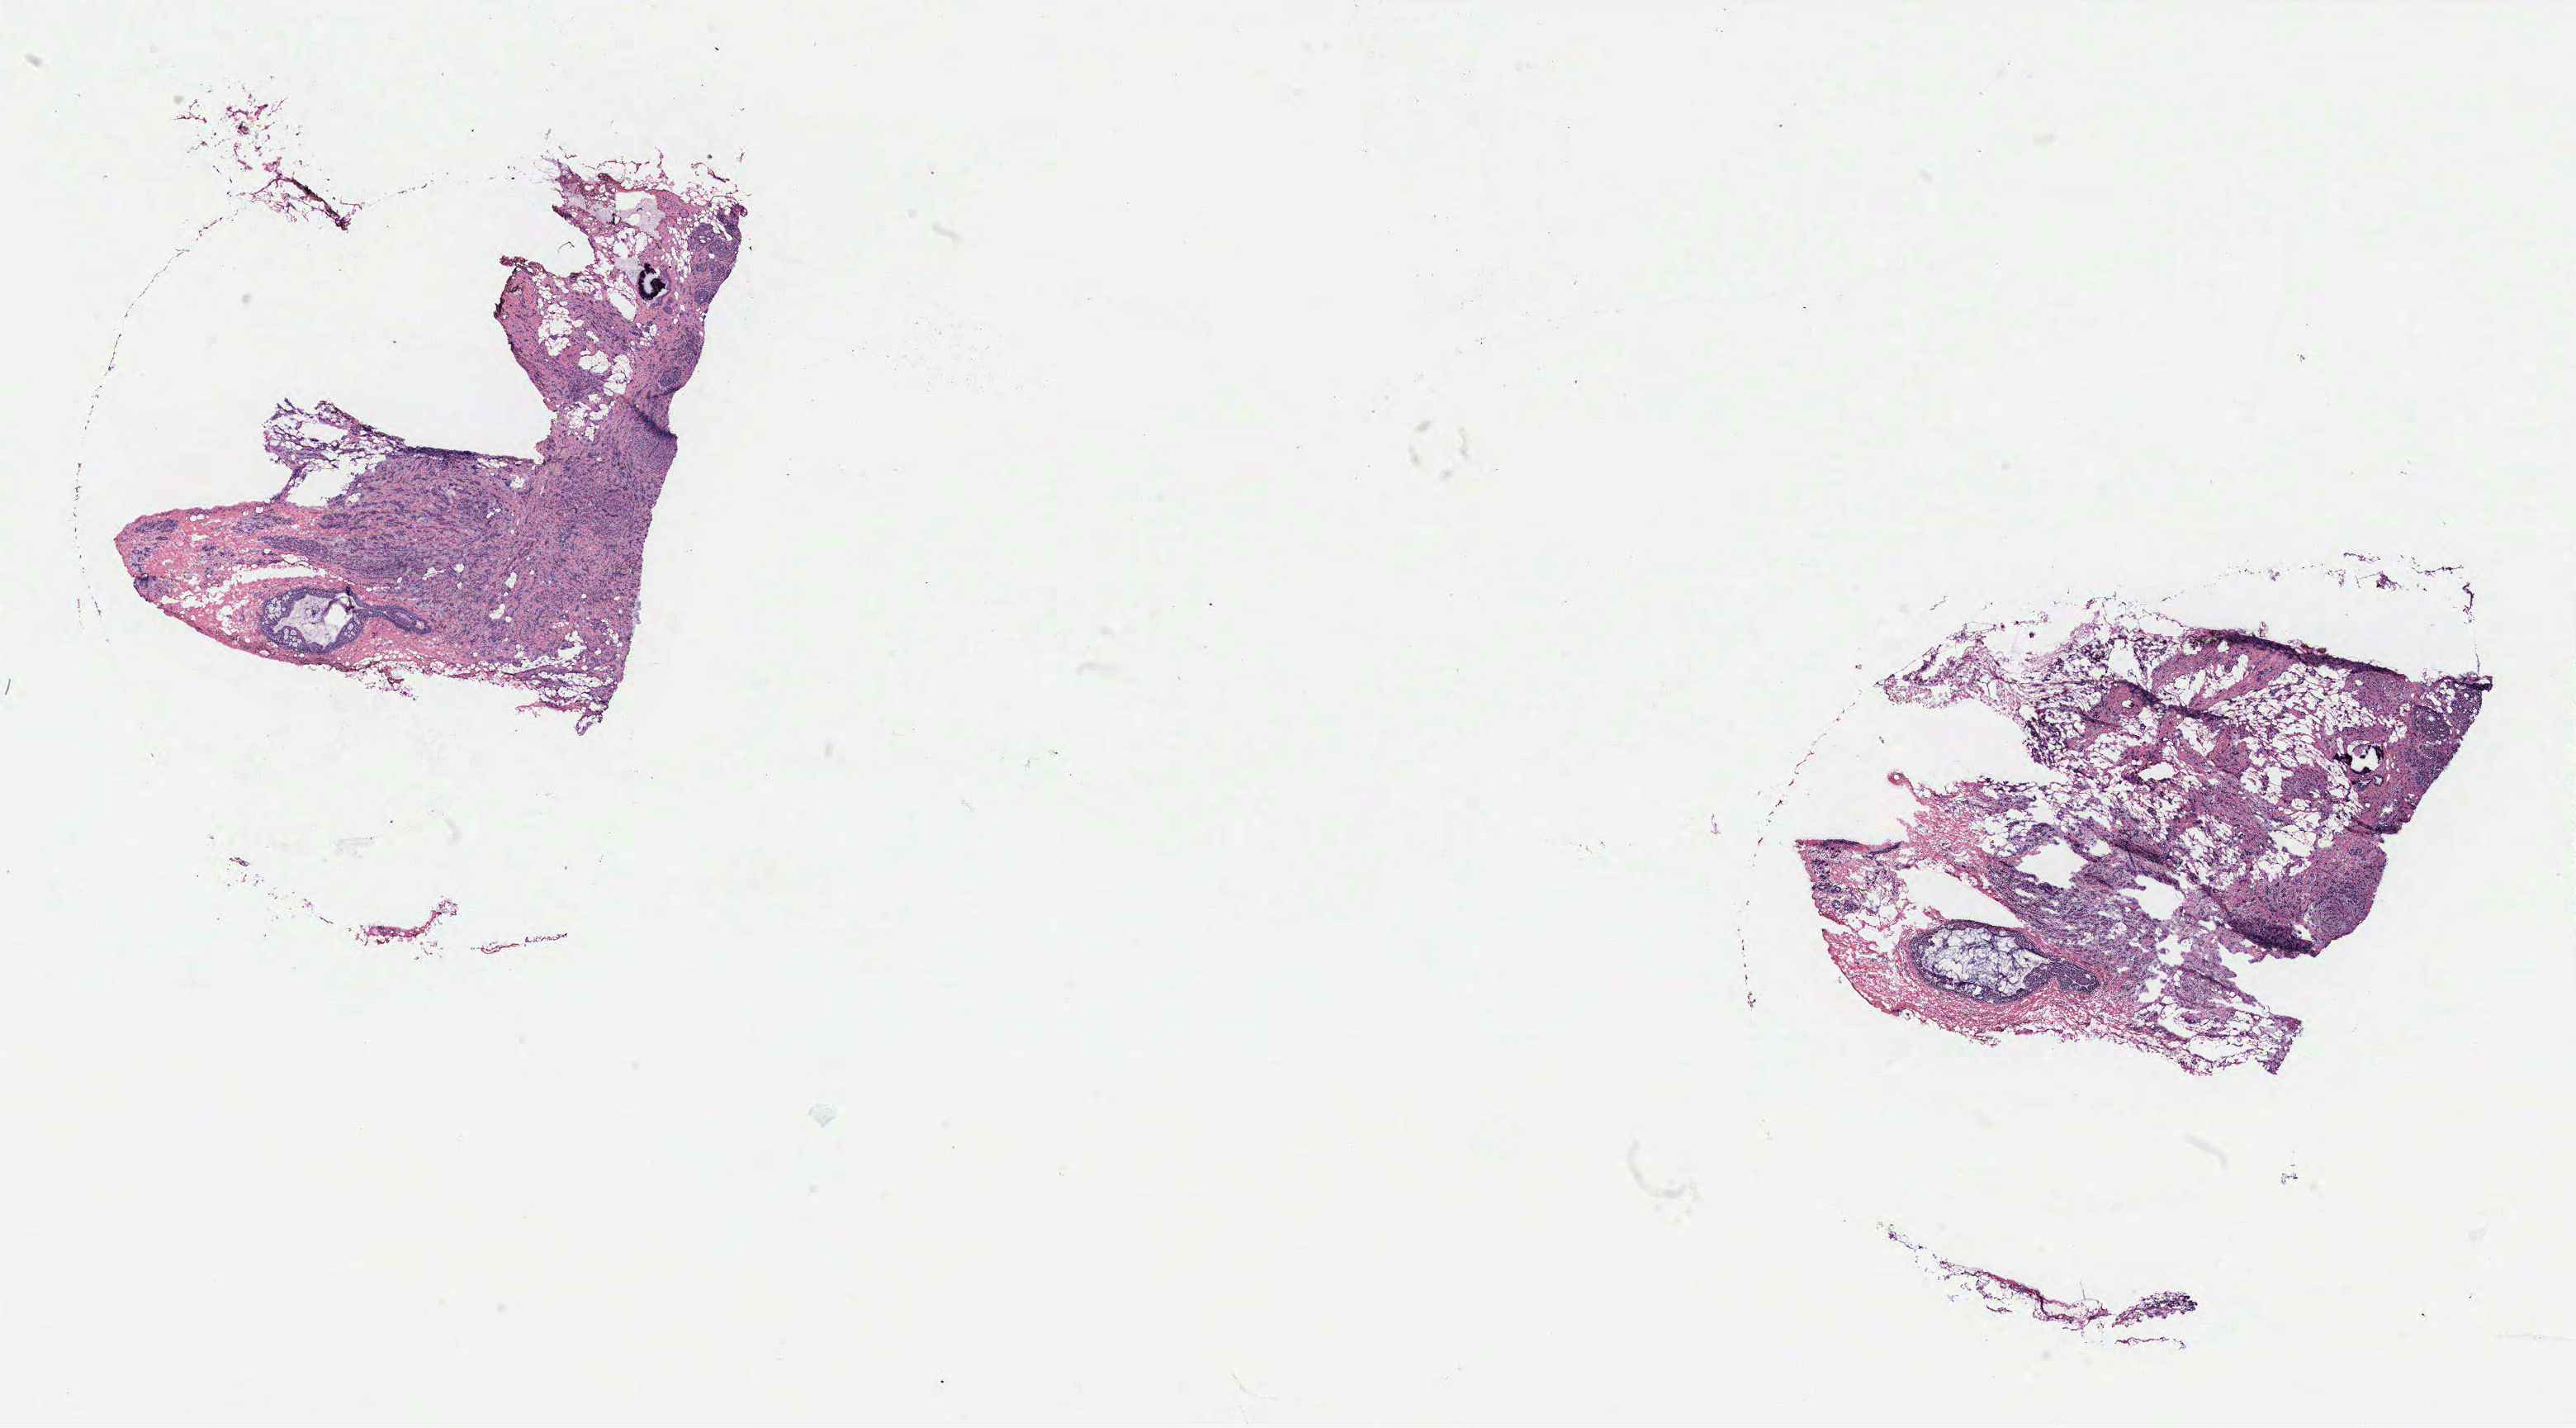
H&E whole-slide image — a low-resolution overview of the entire scanned area, about 25.0 x 13.8 mm (acquisition: 40x scan), breast, tumour tissue. 37-year-old female patient.
Histologic diagnosis: Infiltrating duct carcinoma, NOS. AJCC pathologic stage: IIB.